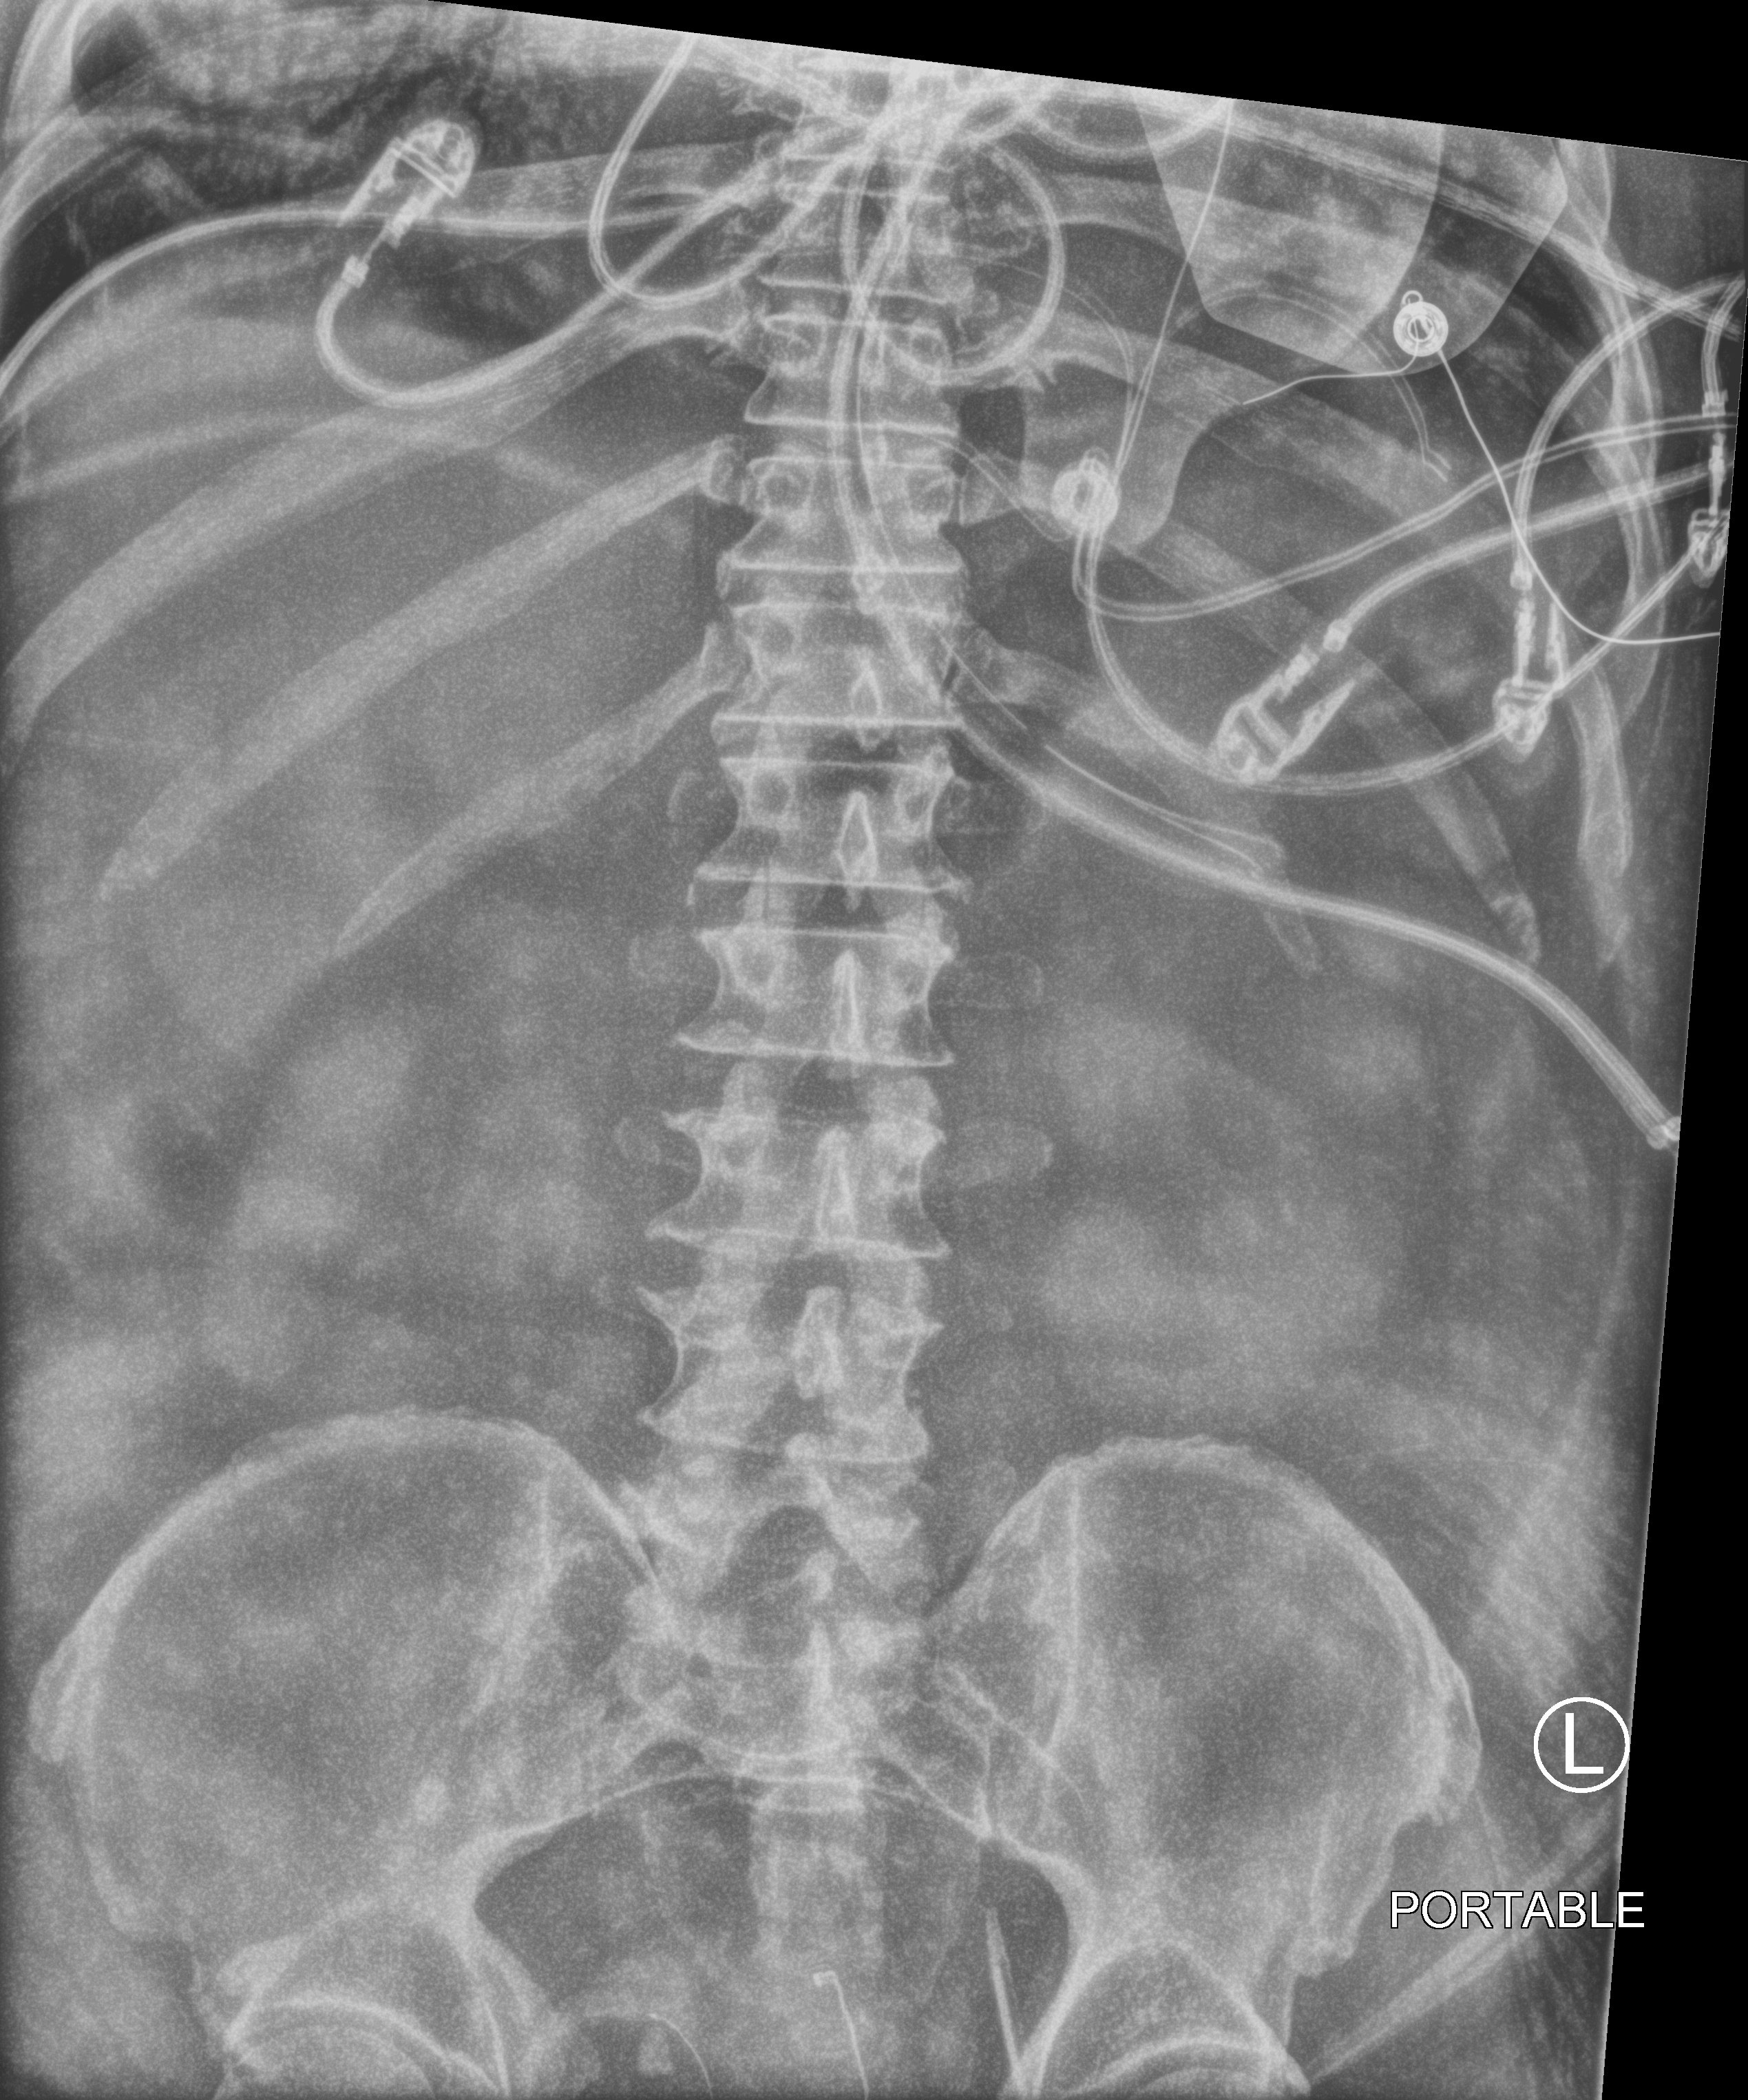
Portable abdomen radiograph, anteroposterior (AP) projection. Patient hospitalised with COVID-19; male, aged 60–74 years.
From the hospital-stay record, not from the radiograph (when in the stay this image was taken is not recorded): mechanically ventilated during this hospital stay: yes.